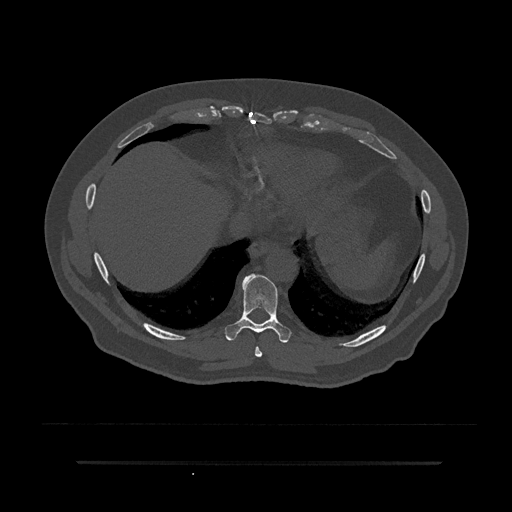
CT including the spine, one axial slice. Position 380 of 797 along the scan axis. Reconstruction kernel Br40s/3. 120 kVp. Bone window (W 1800 / L 400 HU). 0.5 mm slice thickness. 512 × 512 image matrix. Patient: male, 59 years. Case-level facts recorded for this patient, not image findings: primary cancer: bile ducts; vertebrae with lytic lesions (as recorded): T10.
Outlined on this slice (semi-automatic segmentation, software-assisted and operator-edited):
- T8 vertebra: bounding box (x1, y1, x2, y2) in pixels: (255, 346, 263, 357)
- T9 vertebra: (225, 274, 291, 343)